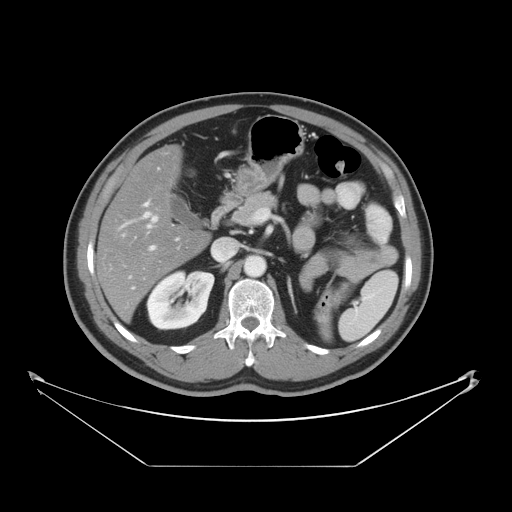
Contrast-enhanced abdominal CT, one axial slice; position 23 of 46 along the scan axis; reconstruction kernel STANDARD; 120 kVp; soft-tissue window (W 400 / L 40 HU); 5 mm slice thickness; 512 × 512 image matrix, field of view 465 × 465 mm. Male patient, age 57 years. From the clinical record (not read from this slice): diagnosis: colorectal cancer liver metastases, imaged before liver resection; multiple liver metastases: no; largest metastasis: 3.3 cm; disease in both lobes: no.
Structures marked on this image (outlined manually by an expert reader):
- hepatic veins: bounding box [x1, y1, x2, y2] px = [144, 212, 157, 228]
- liver: [97, 147, 207, 321]
- planned liver remnant (the part of the liver to remain after resection): [97, 147, 207, 320]
- portal vein (with intrahepatic branches): [144, 202, 155, 250]